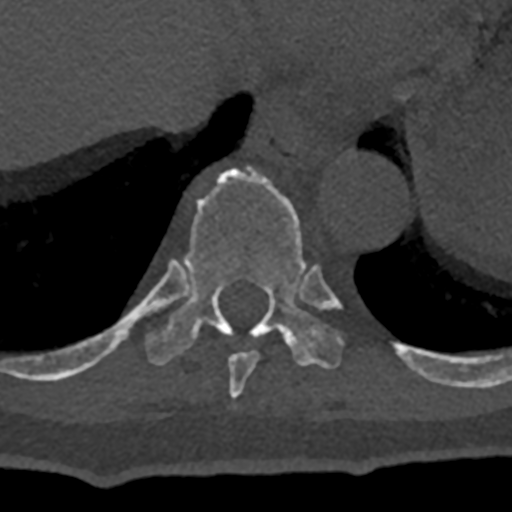
CT including the spine, one axial slice; position 617 of 797 along the scan axis; reconstruction kernel Br40s/3; bone window (W 1800 / L 400 HU); 0.5 mm slice thickness; 512 × 512 image matrix, field of view 160 × 160 mm. Male patient, age 74 years. From the clinical record (not read from this slice): primary cancer: renal.
Structures marked on this image (semi-automatically segmented with operator editing):
- T10 vertebra: bounding box <70,166,432,381> (left, top, right, bottom; pixels)
- T9 vertebra: <228,351,259,399>